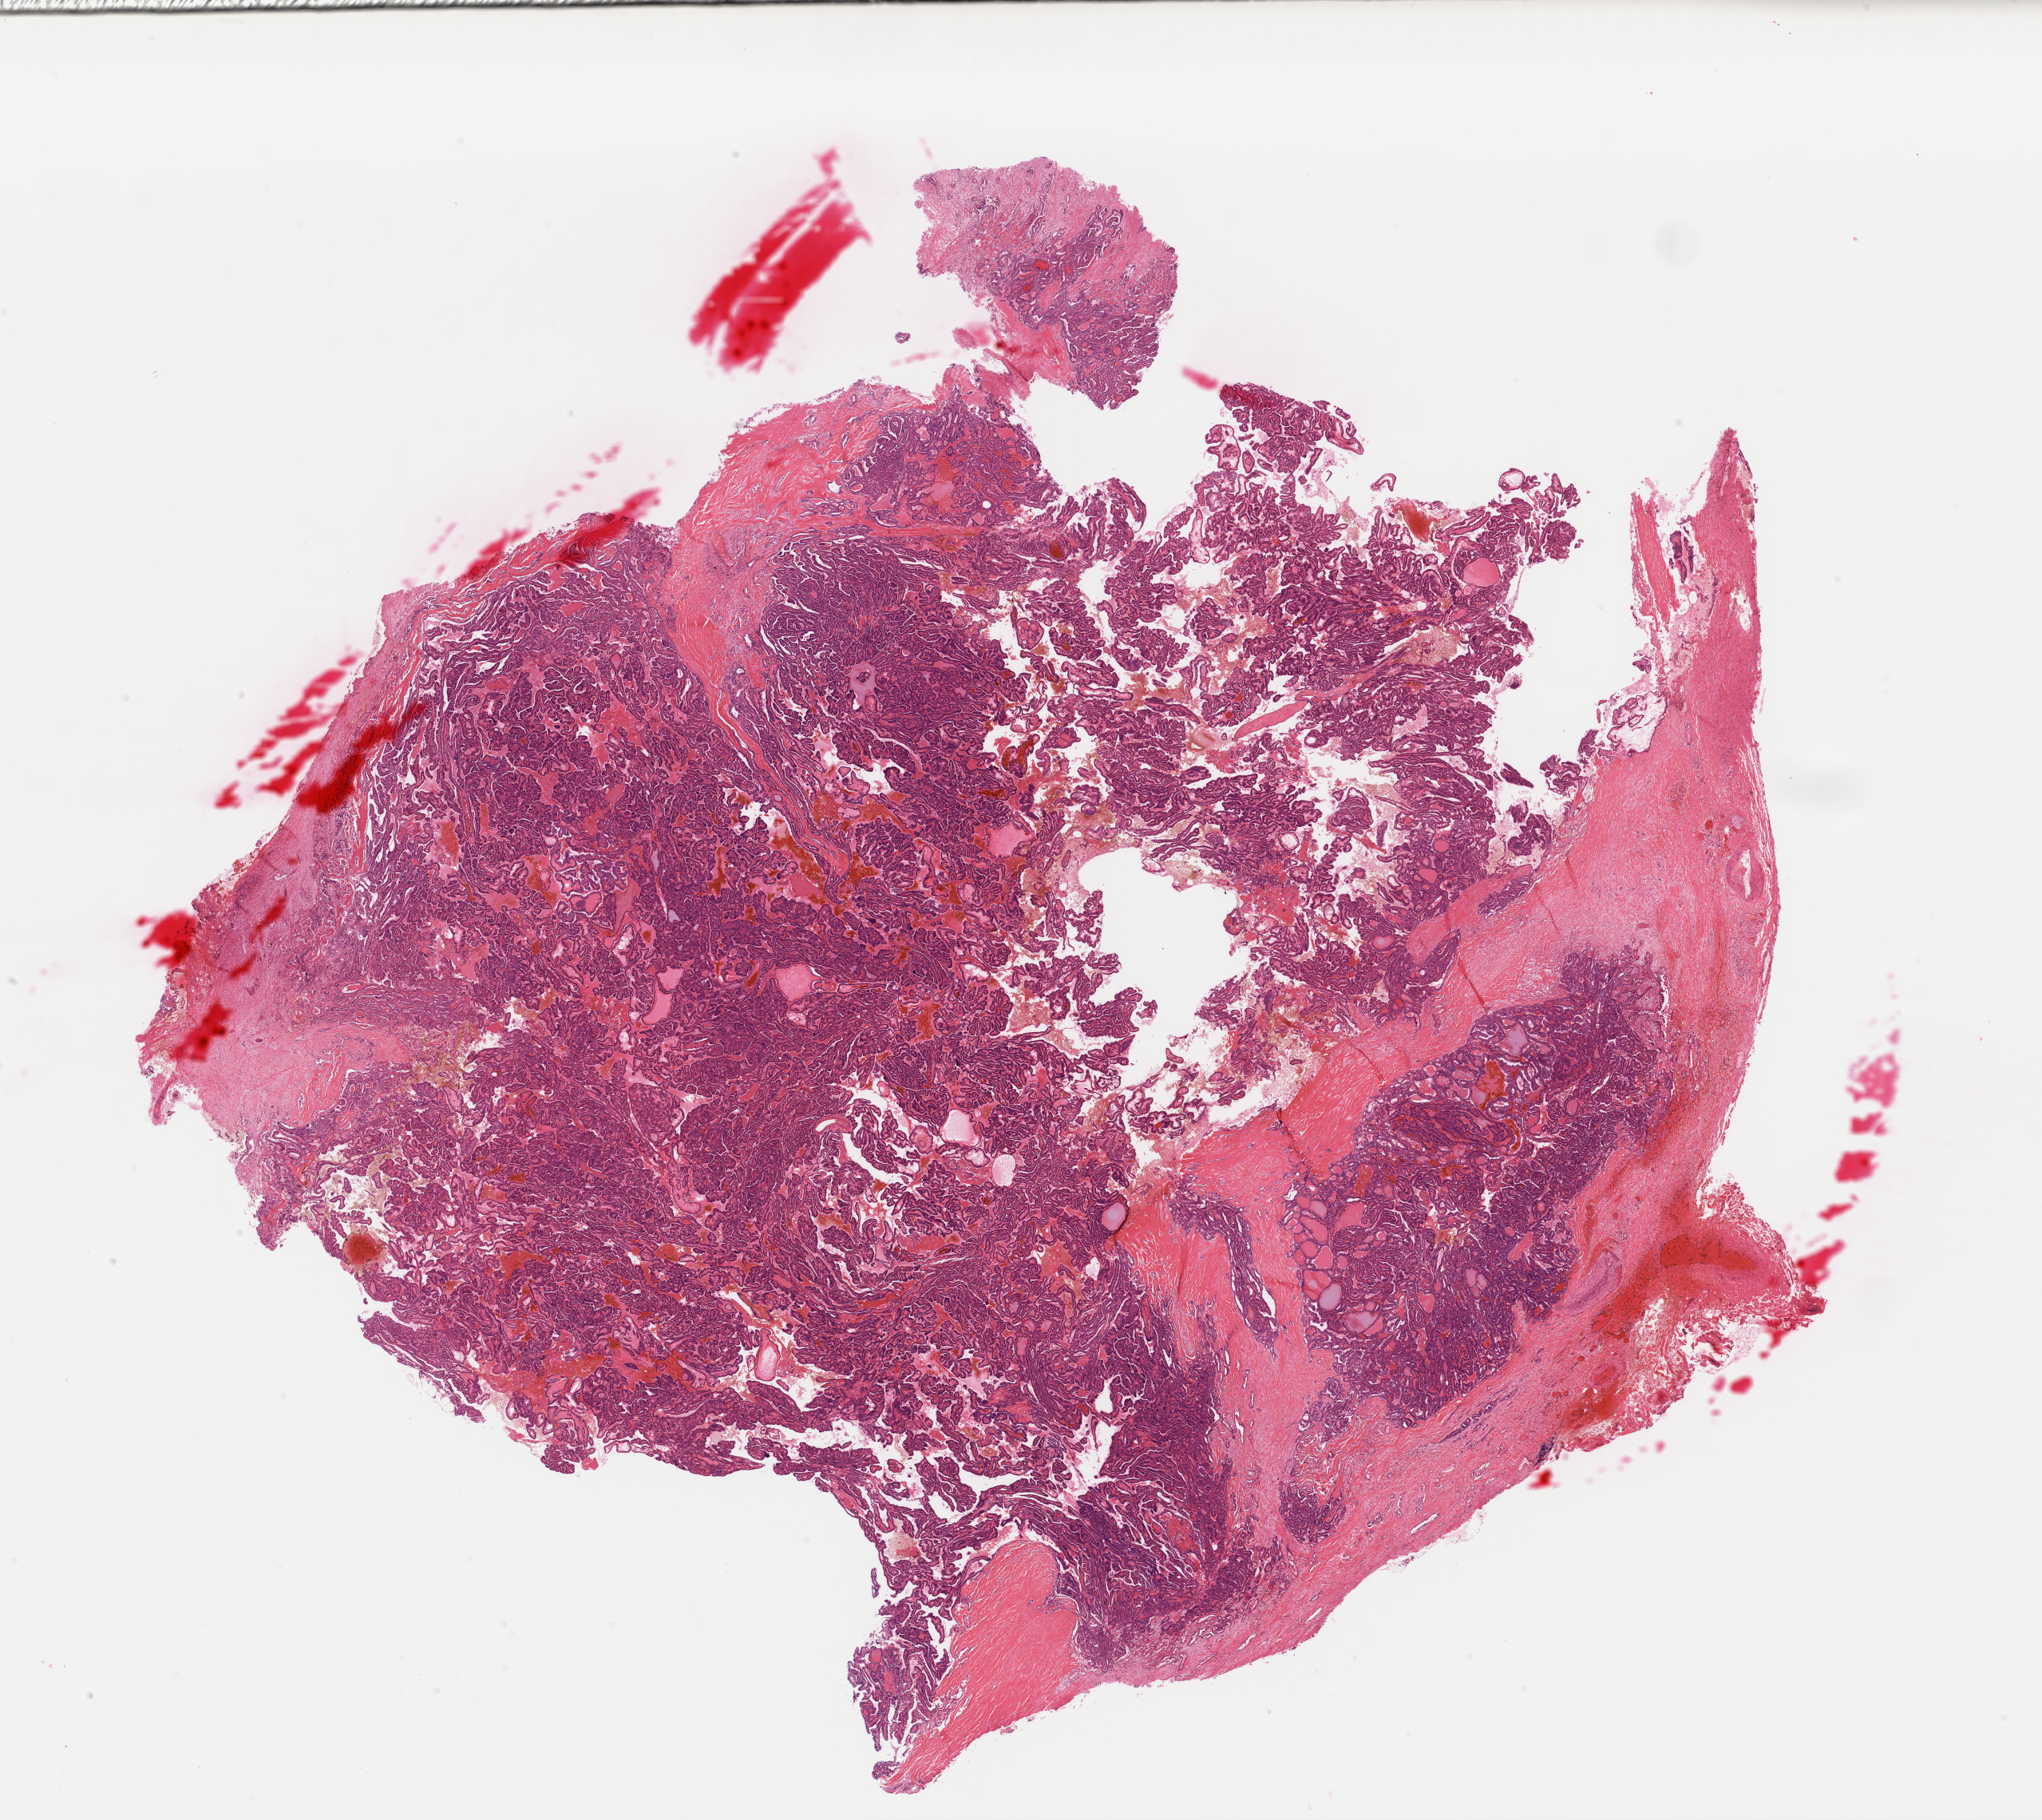
Digitized H&E-stained tissue section (whole slide) — low-resolution overview of the scanned area, about 20.2 x 18.0 mm. FFPE section. Primary tumour sample from the thyroid. Female, age 45 years at initial diagnosis.
* AJCC pathologic stage: III (7th edition)
* lymph nodes positive (case pathology): 0 of 1 examined
* diagnosis: Papillary adenocarcinoma, NOS (thyroid gland)